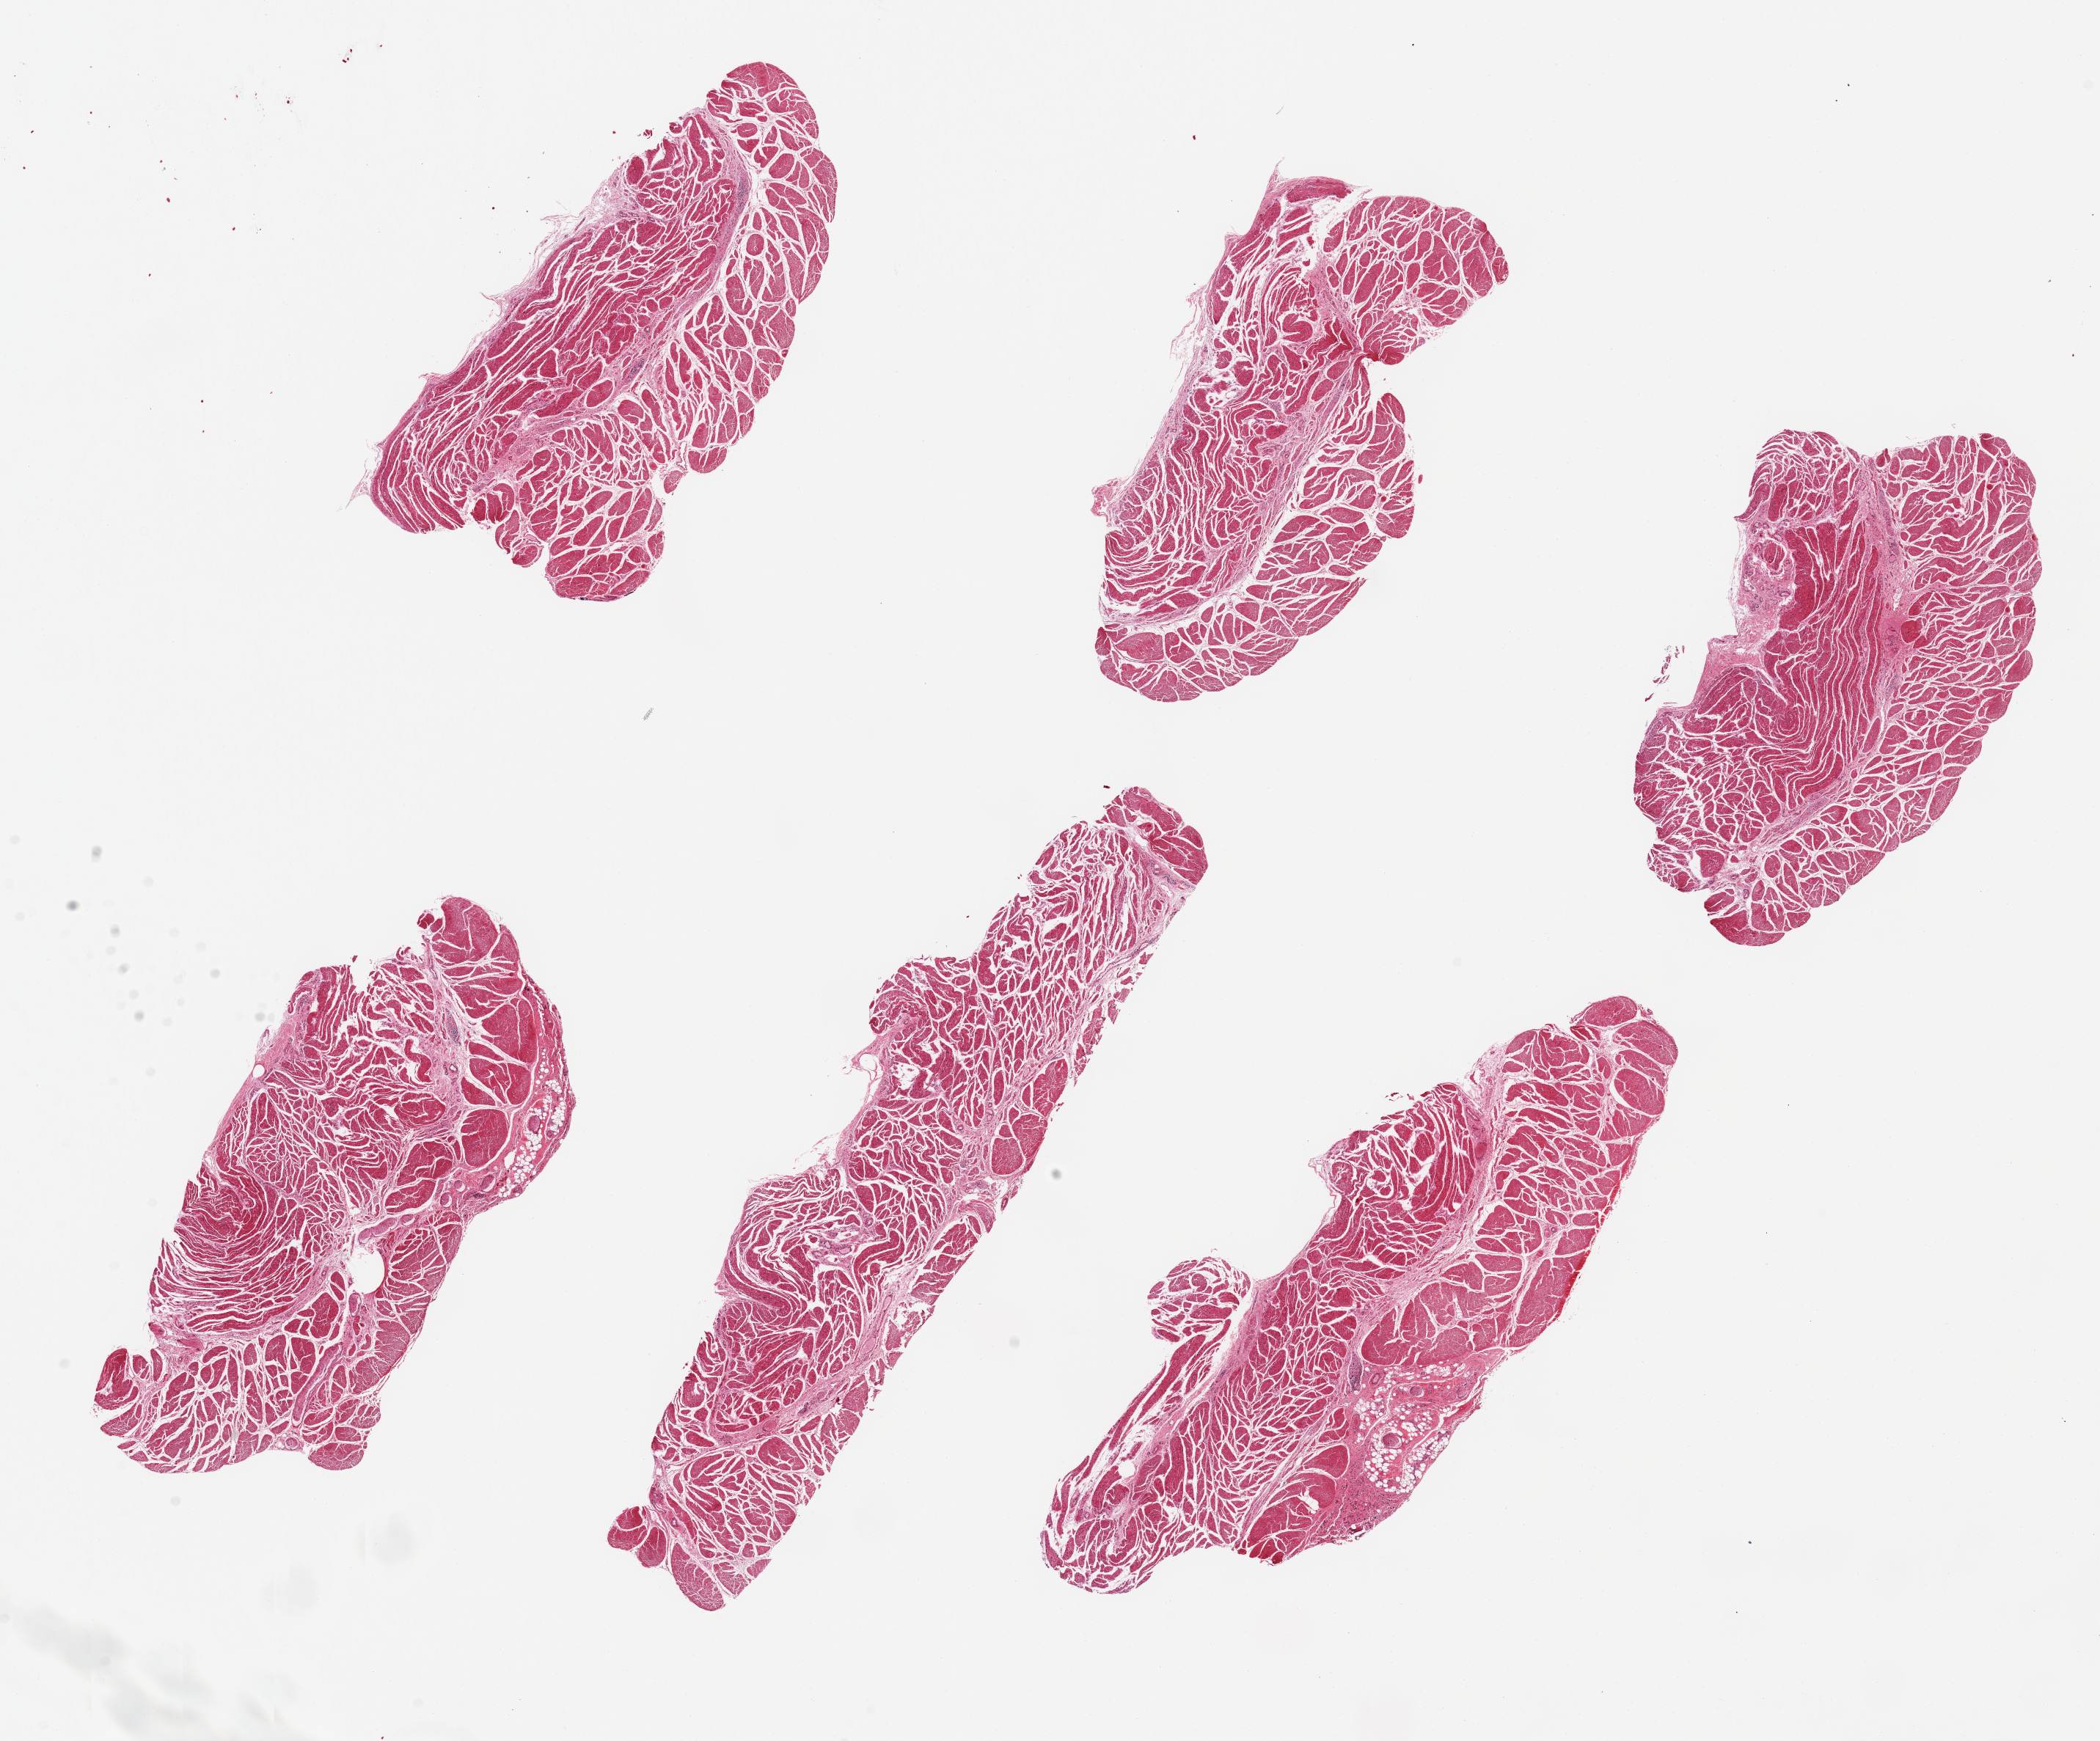
Whole-slide image, H&E stain — shown as a low-resolution overview of the whole scanned area (about 22.6 x 18.8 mm); PAXgene-fixed, paraffin-embedded tissue; section of esophageal muscle (target tissue); tissue donor sample. Male donor.
Pathologist's review note for this sample: 6 pieces, up to 10x2.5mm; all muscle.